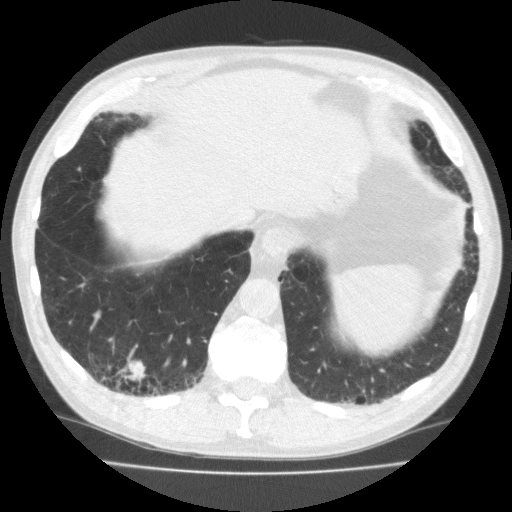
Low-dose screening chest CT, one axial slice. Slice 51 of 195 in the series (ordered by position). Lung window (W 1500 / L -600 HU). 2 mm slice thickness. 512 × 512 image matrix, field of view 350 × 350 mm.
Outlined on this slice (expert manual segmentation):
- lesion 1 (tumor, lower lobe of right lung): bounding box [x1, y1, x2, y2] px = [121, 360, 147, 383]